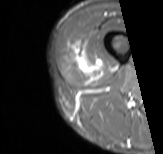
MRI of an extremity soft-tissue mass, one axial slice; position 11 of 61 along the scan axis; STIR; MR volume resampled by the dataset authors to the PET/CT grid (not the native acquisition matrix); 3.27 mm slice thickness; 163 × 154 image matrix. Male patient. From the clinical record (not read from this slice): histological type: poorly differentiated synovial sarcoma; grade: high; site of the primary tumour: right buttock.
Structures marked on this image (expert contour drawn on MRI and transferred to this co-registered scan by the dataset authors):
- gross tumour volume including surrounding oedema: bounding box <75,44,99,72> (left, top, right, bottom; pixels)